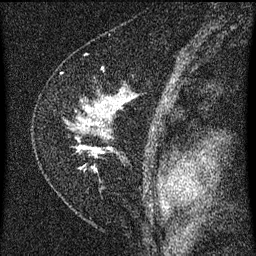
Breast MRI (dynamic contrast-enhanced), one sagittal slice. Position 42 of 60 along the scan axis. Dynamic contrast-enhanced series, image 2 of 3 at this slice position (ordered by acquisition). 1.5 T. TE 4.2 ms, TR 8 ms. 2 mm slice thickness. 256 × 256 image matrix, field of view 180 × 180 mm. Patient: female, 47 years.
Structures marked on this image (semi-automatically segmented with operator editing):
- analysis volume of interest (the breast-tissue region the enhancement analysis was run in; not a lesion): box from (x=64, y=90) to (x=134, y=173) px
- tumour enhancement mask (voxels above the 70 % enhancement threshold inside the analysis volume of interest): (x=79, y=102)–(x=125, y=153)